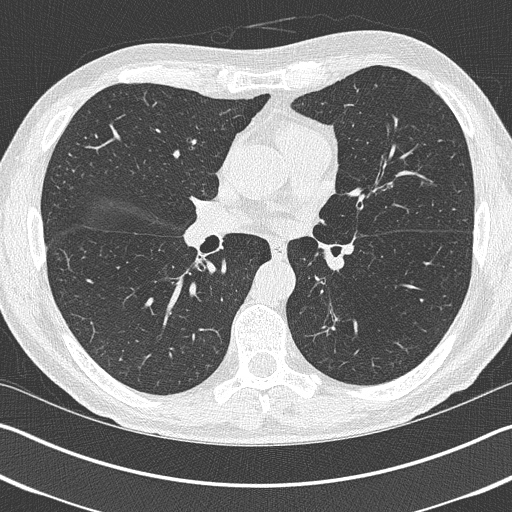
Axial slice from a low-dose chest CT screening exam. First (baseline) screen. Lung window (W 1500 / L -600 HU). Lung (sharp) reconstruction kernel (B50f). 120 kVp. Male participant, aged 69 years at enrolment.
Lesion marked by an expert reader, bounding box <292,304,349,364> (left, top, right, bottom; pixels). Screening reader's record for this exam (one nodule recorded; not confirmed to be the boxed lesion): non-calcified nodule or mass ≥4 mm, left upper lobe, 19 × 19 mm, spiculated (stellate) margins, pre-existing on the prior screen: yes. Lung cancer was diagnosed 202 days after this screen: non-small cell carcinoma, left lower lobe, stage IIIA (AJCC 6th edition), 20 mm at pathology.